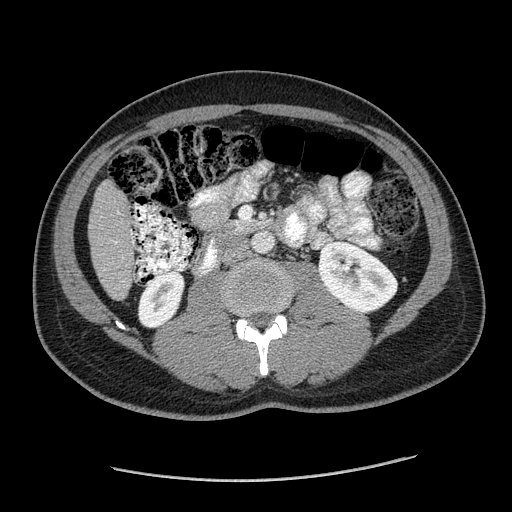
Contrast-enhanced abdominal CT (liver protocol), one axial slice; position 41 of 182 along the scan axis; reconstruction kernel STANDARD; soft-tissue window (W 400 / L 40 HU); 2.5 mm slice thickness; 512 × 512 image matrix, field of view 400 × 400 mm. From the clinical record (not read from this slice): diagnosis: hepatocellular carcinoma (patient treated with transarterial chemoembolisation; whether this scan precedes or follows treatment is not stated here); TNM stage (as recorded): Stage-I; Child-Pugh class: A; tumour differentiation: well differentiated.
Structures marked on this image (semi-automatically segmented with operator editing):
- liver parenchyma outside the tumour (the mass and vessels are separate outlines, so this box may not span the whole liver): bounding box [x1, y1, x2, y2] px = [88, 180, 134, 298]